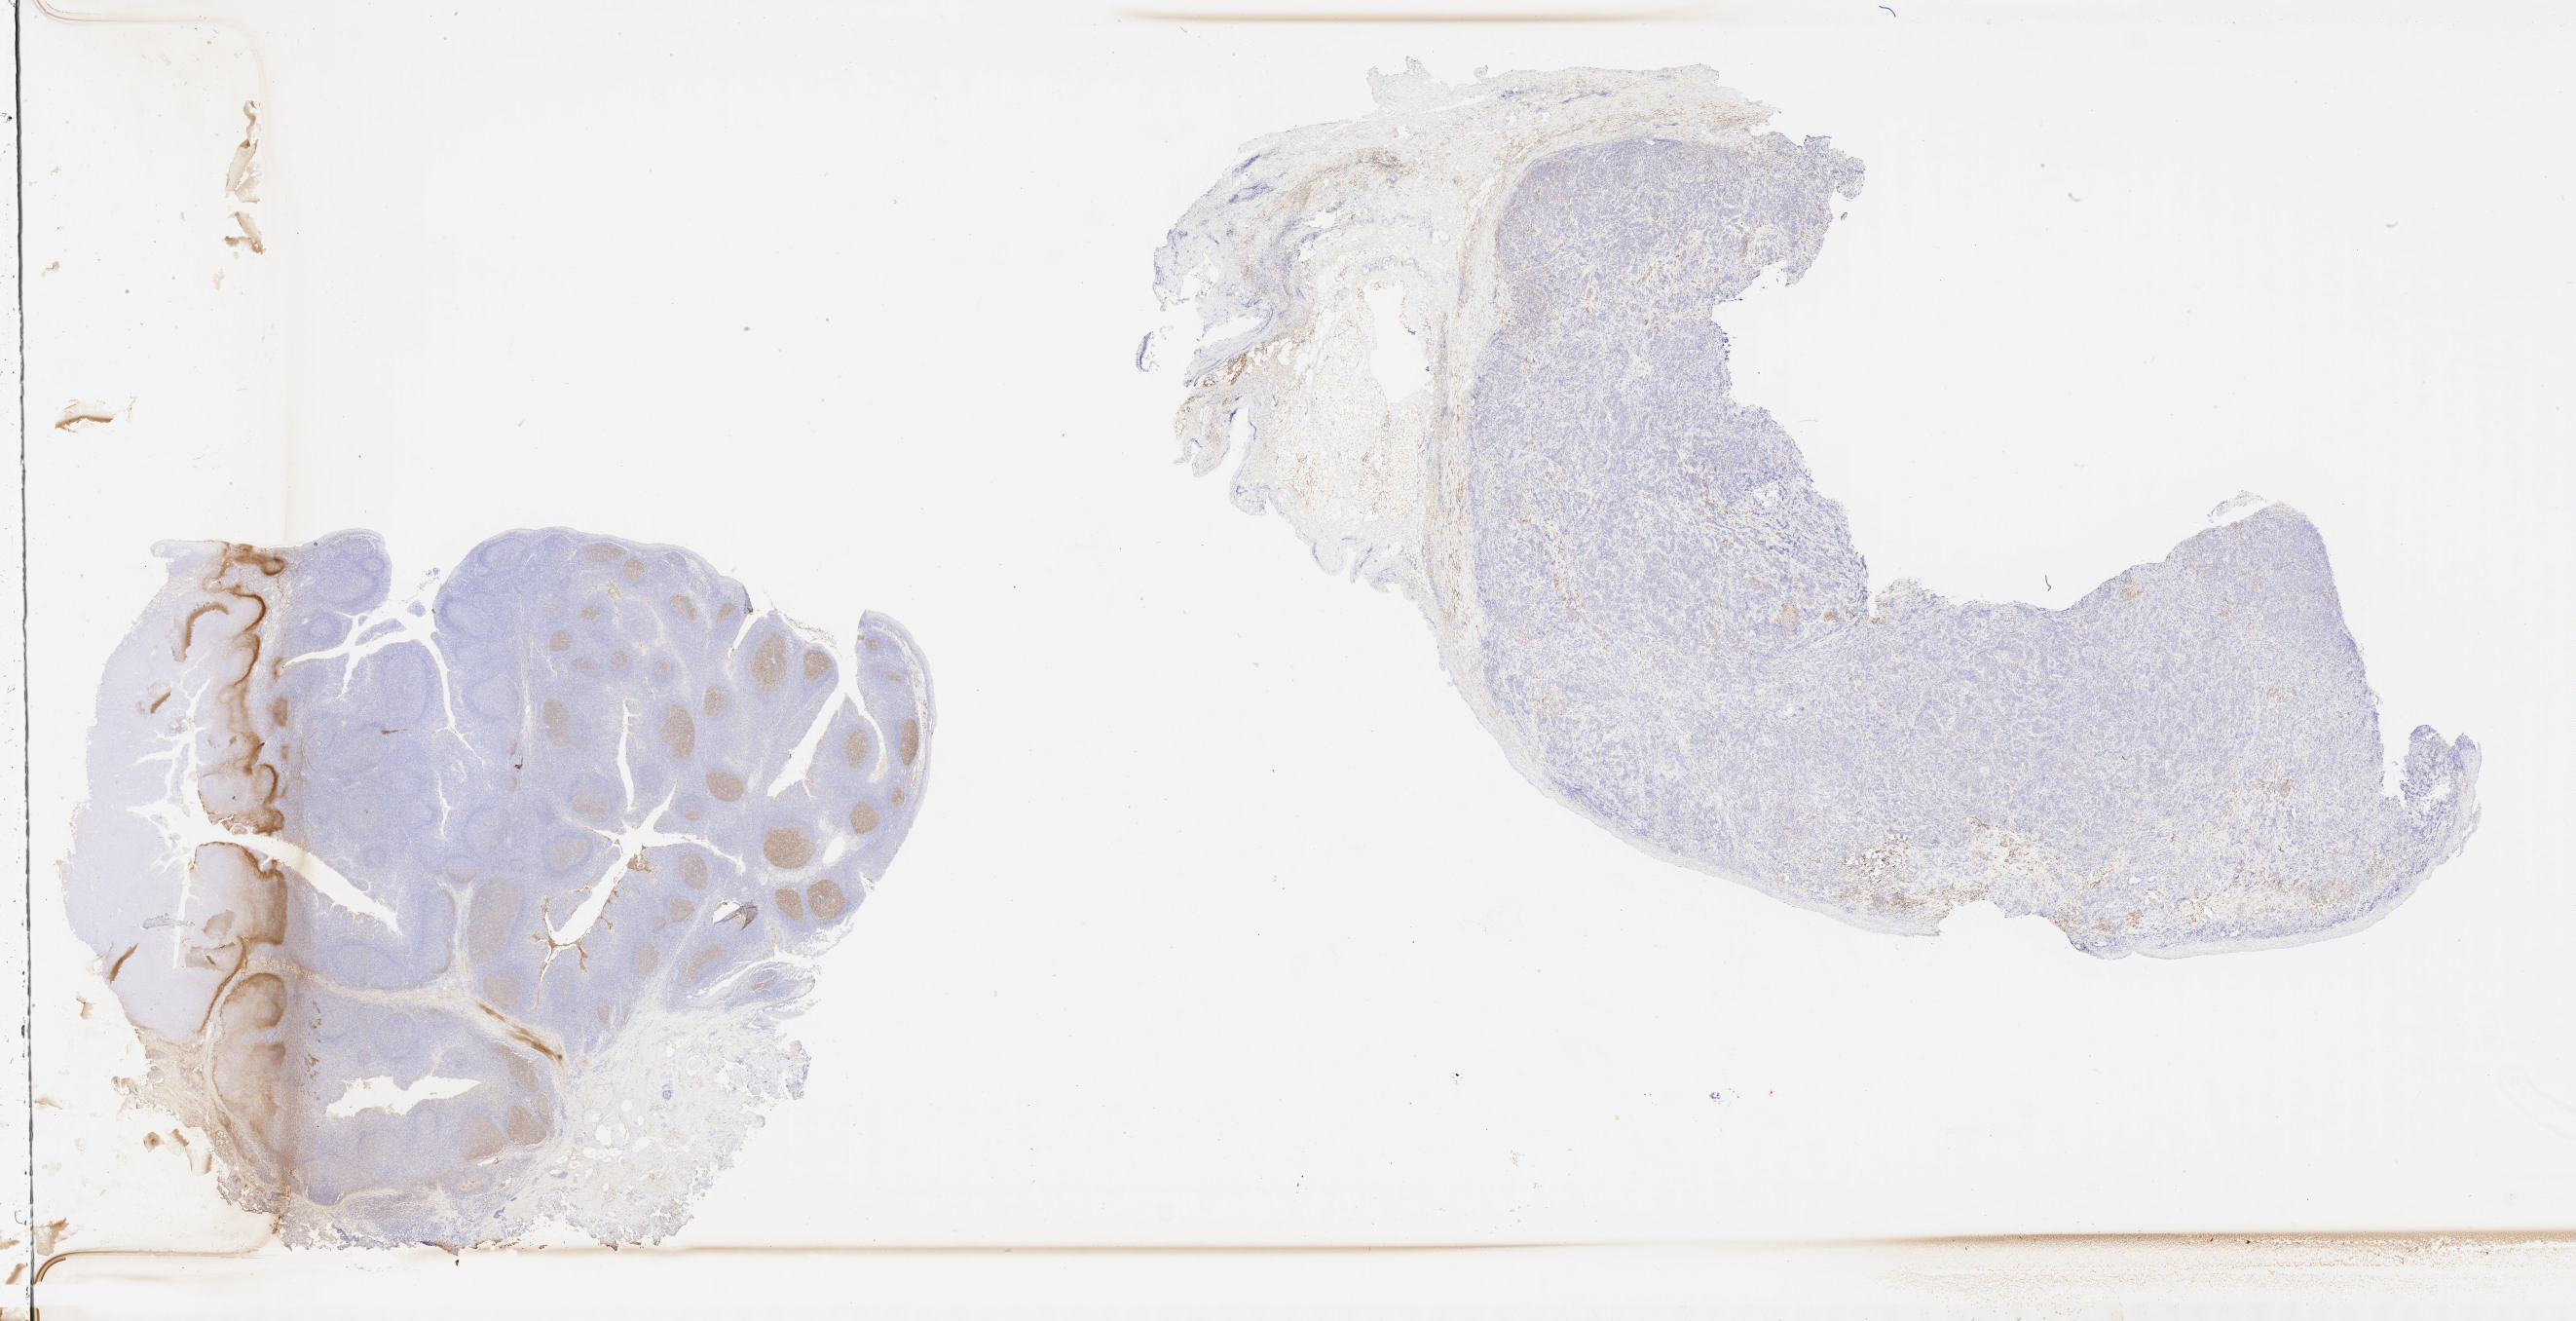
IHC for CD10, whole-slide image, shown as a low-resolution overview of the whole scanned area (about 42.8 x 21.9 mm), tumor tissue, site: bone. Patient: male, 48 years old.
Diagnosis: Diffuse large B-cell lymphoma, NOS.